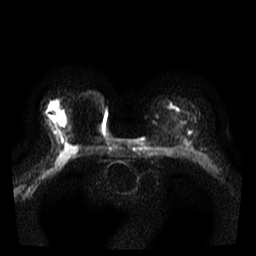
Breast MRI, one axial slice; position 24 of 35 along the scan axis; diffusion-weighted series; image 2 of 4 stored at this slice position (different b-values; order by instance number); 3 T; 256 × 256 image matrix, field of view 300 × 300 mm. Female patient.
Annotated regions visible in this slice (expert manual segmentation):
- tumour on diffusion-weighted imaging: bounding box [x1, y1, x2, y2] px = [52, 116, 55, 119]